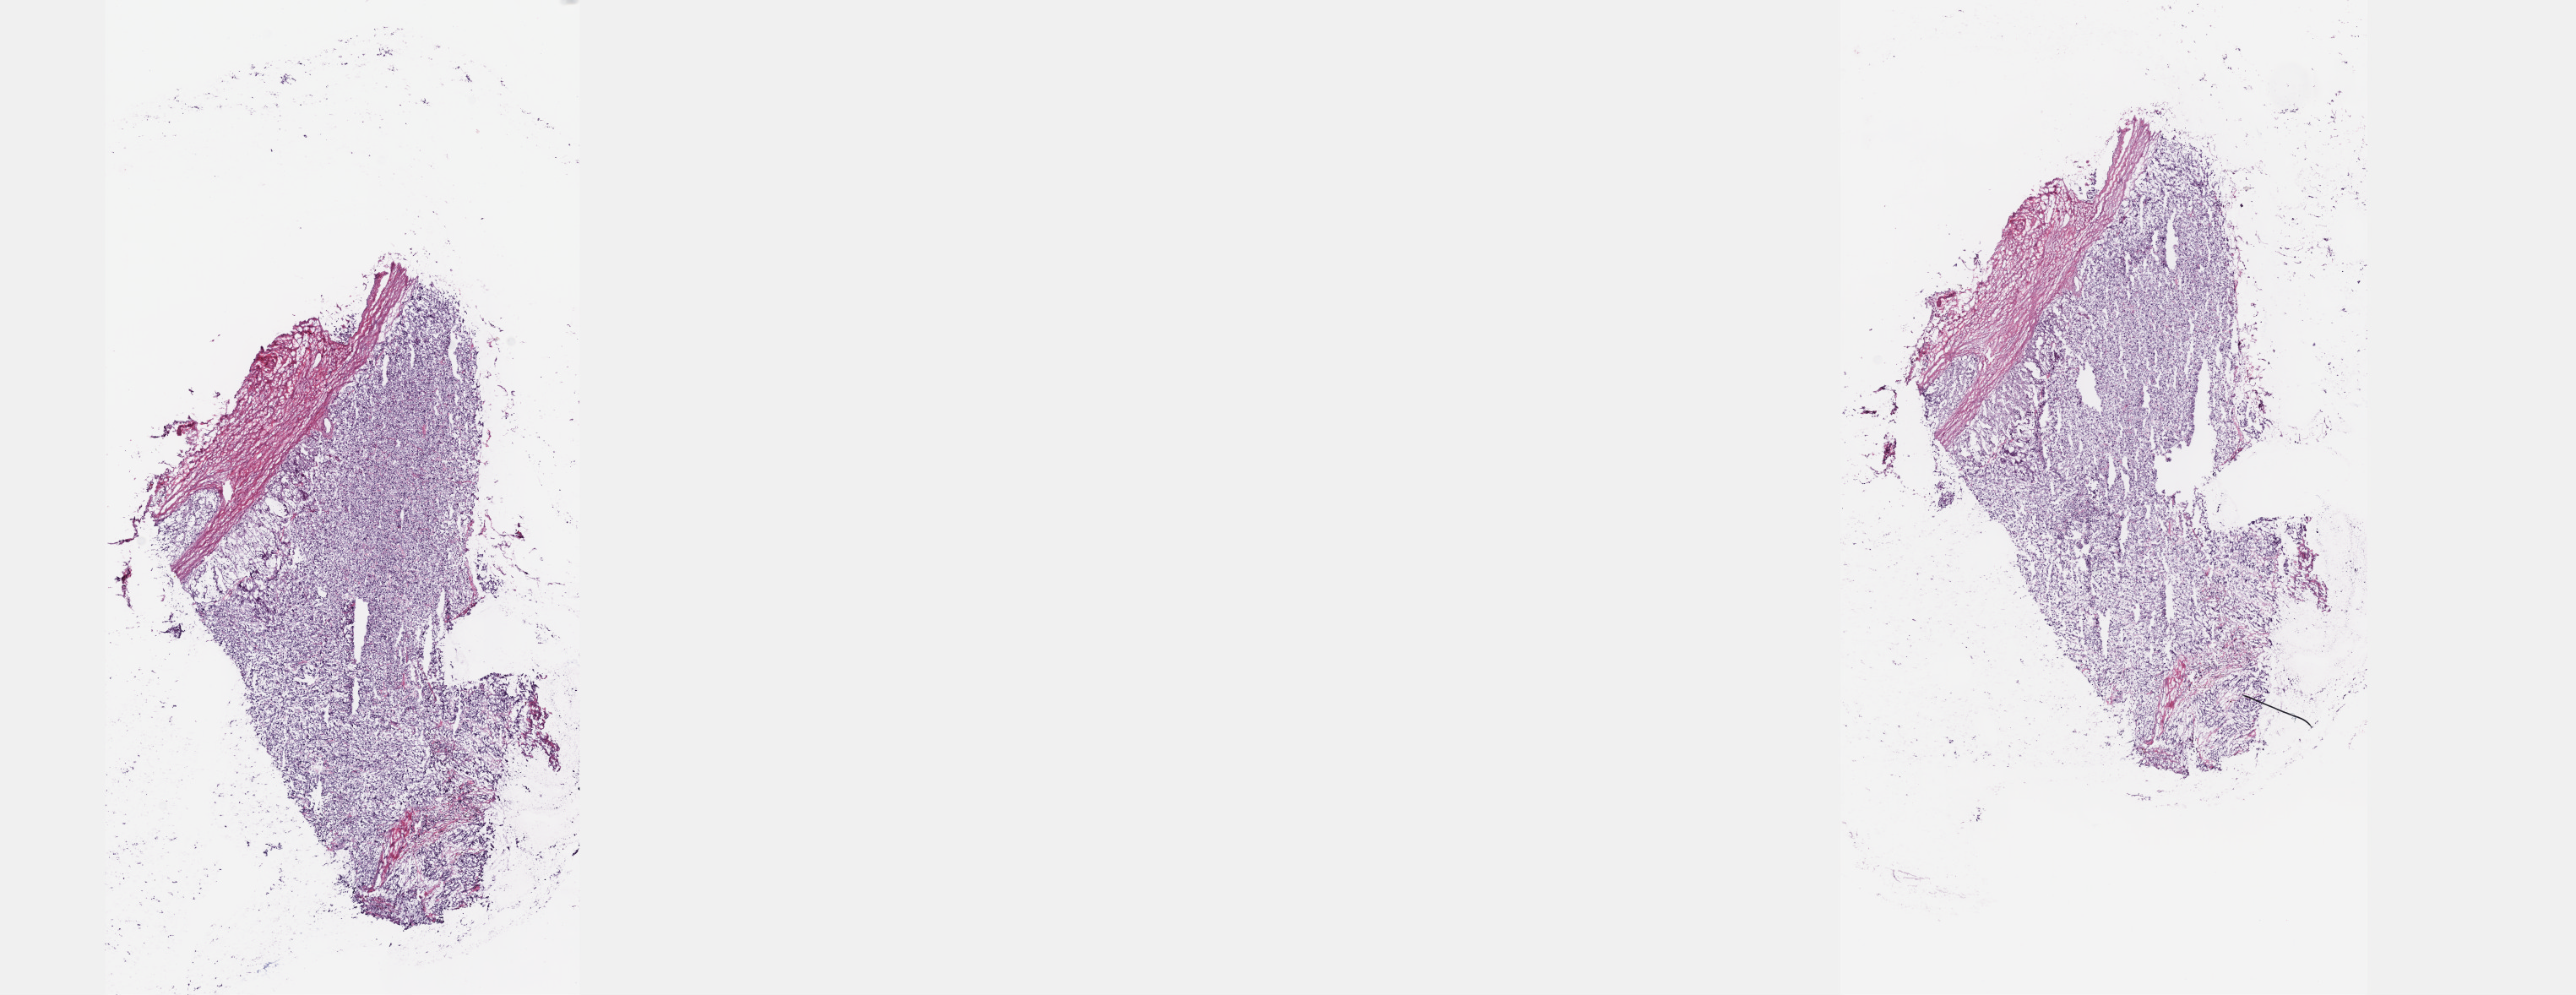
Whole-slide histology image, Hematoxylin and eosin (H&E) stained, shown as a low-resolution overview of the whole scanned area (about 24.6 x 9.5 mm, from a 40x scan). Frozen section from the top of the tissue portion. Primary tumour sample from the adrenal gland. Male patient; age at initial diagnosis 52 years. Slide review estimates, as recorded: tumour cells 100%, tumour nuclei 80%, normal cells 0%, stromal cells 0%, necrosis 0%. Infiltration values recorded for this section: lymphocyte infiltration 2%, monocyte infiltration 0%, neutrophil infiltration 0%.
Laterality: right. Histologic diagnosis: Pheochromocytoma, malignant.